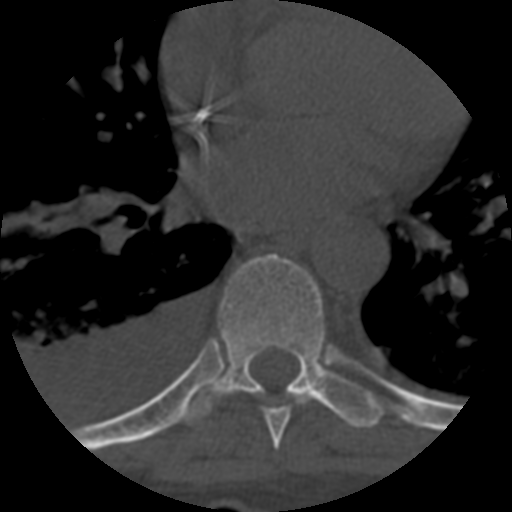
CT including the spine, one axial slice. Slice 403 of 708 in the series (ordered by position). 120 kVp. One of 3 acquisitions stored at this slice position. Bone window (W 1800 / L 400 HU). 1.25 mm slice thickness. 512 × 512 image matrix, field of view 160 × 160 mm. Patient age 55 years. From the clinical record (not read from this slice): primary cancer: colon.
Structures marked on this image (semi-automatically segmented with operator editing):
- T7 vertebra: box from (x=263, y=398) to (x=309, y=449) px
- T8 vertebra: (x=185, y=254)–(x=382, y=428)